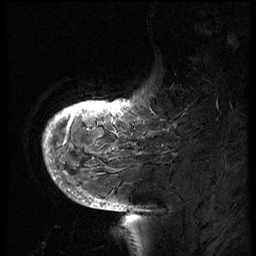
Breast MRI (dynamic contrast-enhanced), one sagittal slice; position 11 of 66 along the scan axis; 3 images stored at this slice position (order not interpretable as contrast timing); 1.5 T; TE 4.2 ms, TR 8.9 ms; 256 × 256 image matrix. Female patient, age 56 years. From the clinical record (not read from this slice): setting: breast cancer imaged before/during neoadjuvant chemotherapy.
Outlined on this slice (semi-automatic segmentation, software-assisted and operator-edited):
- analysis volume of interest (the breast-tissue region the enhancement analysis was run in; not a lesion): bounding box [x1, y1, x2, y2] px = [129, 62, 194, 127]
- tumour enhancement mask (voxels above the 140 % enhancement threshold inside the analysis volume of interest): [129, 101, 135, 108]